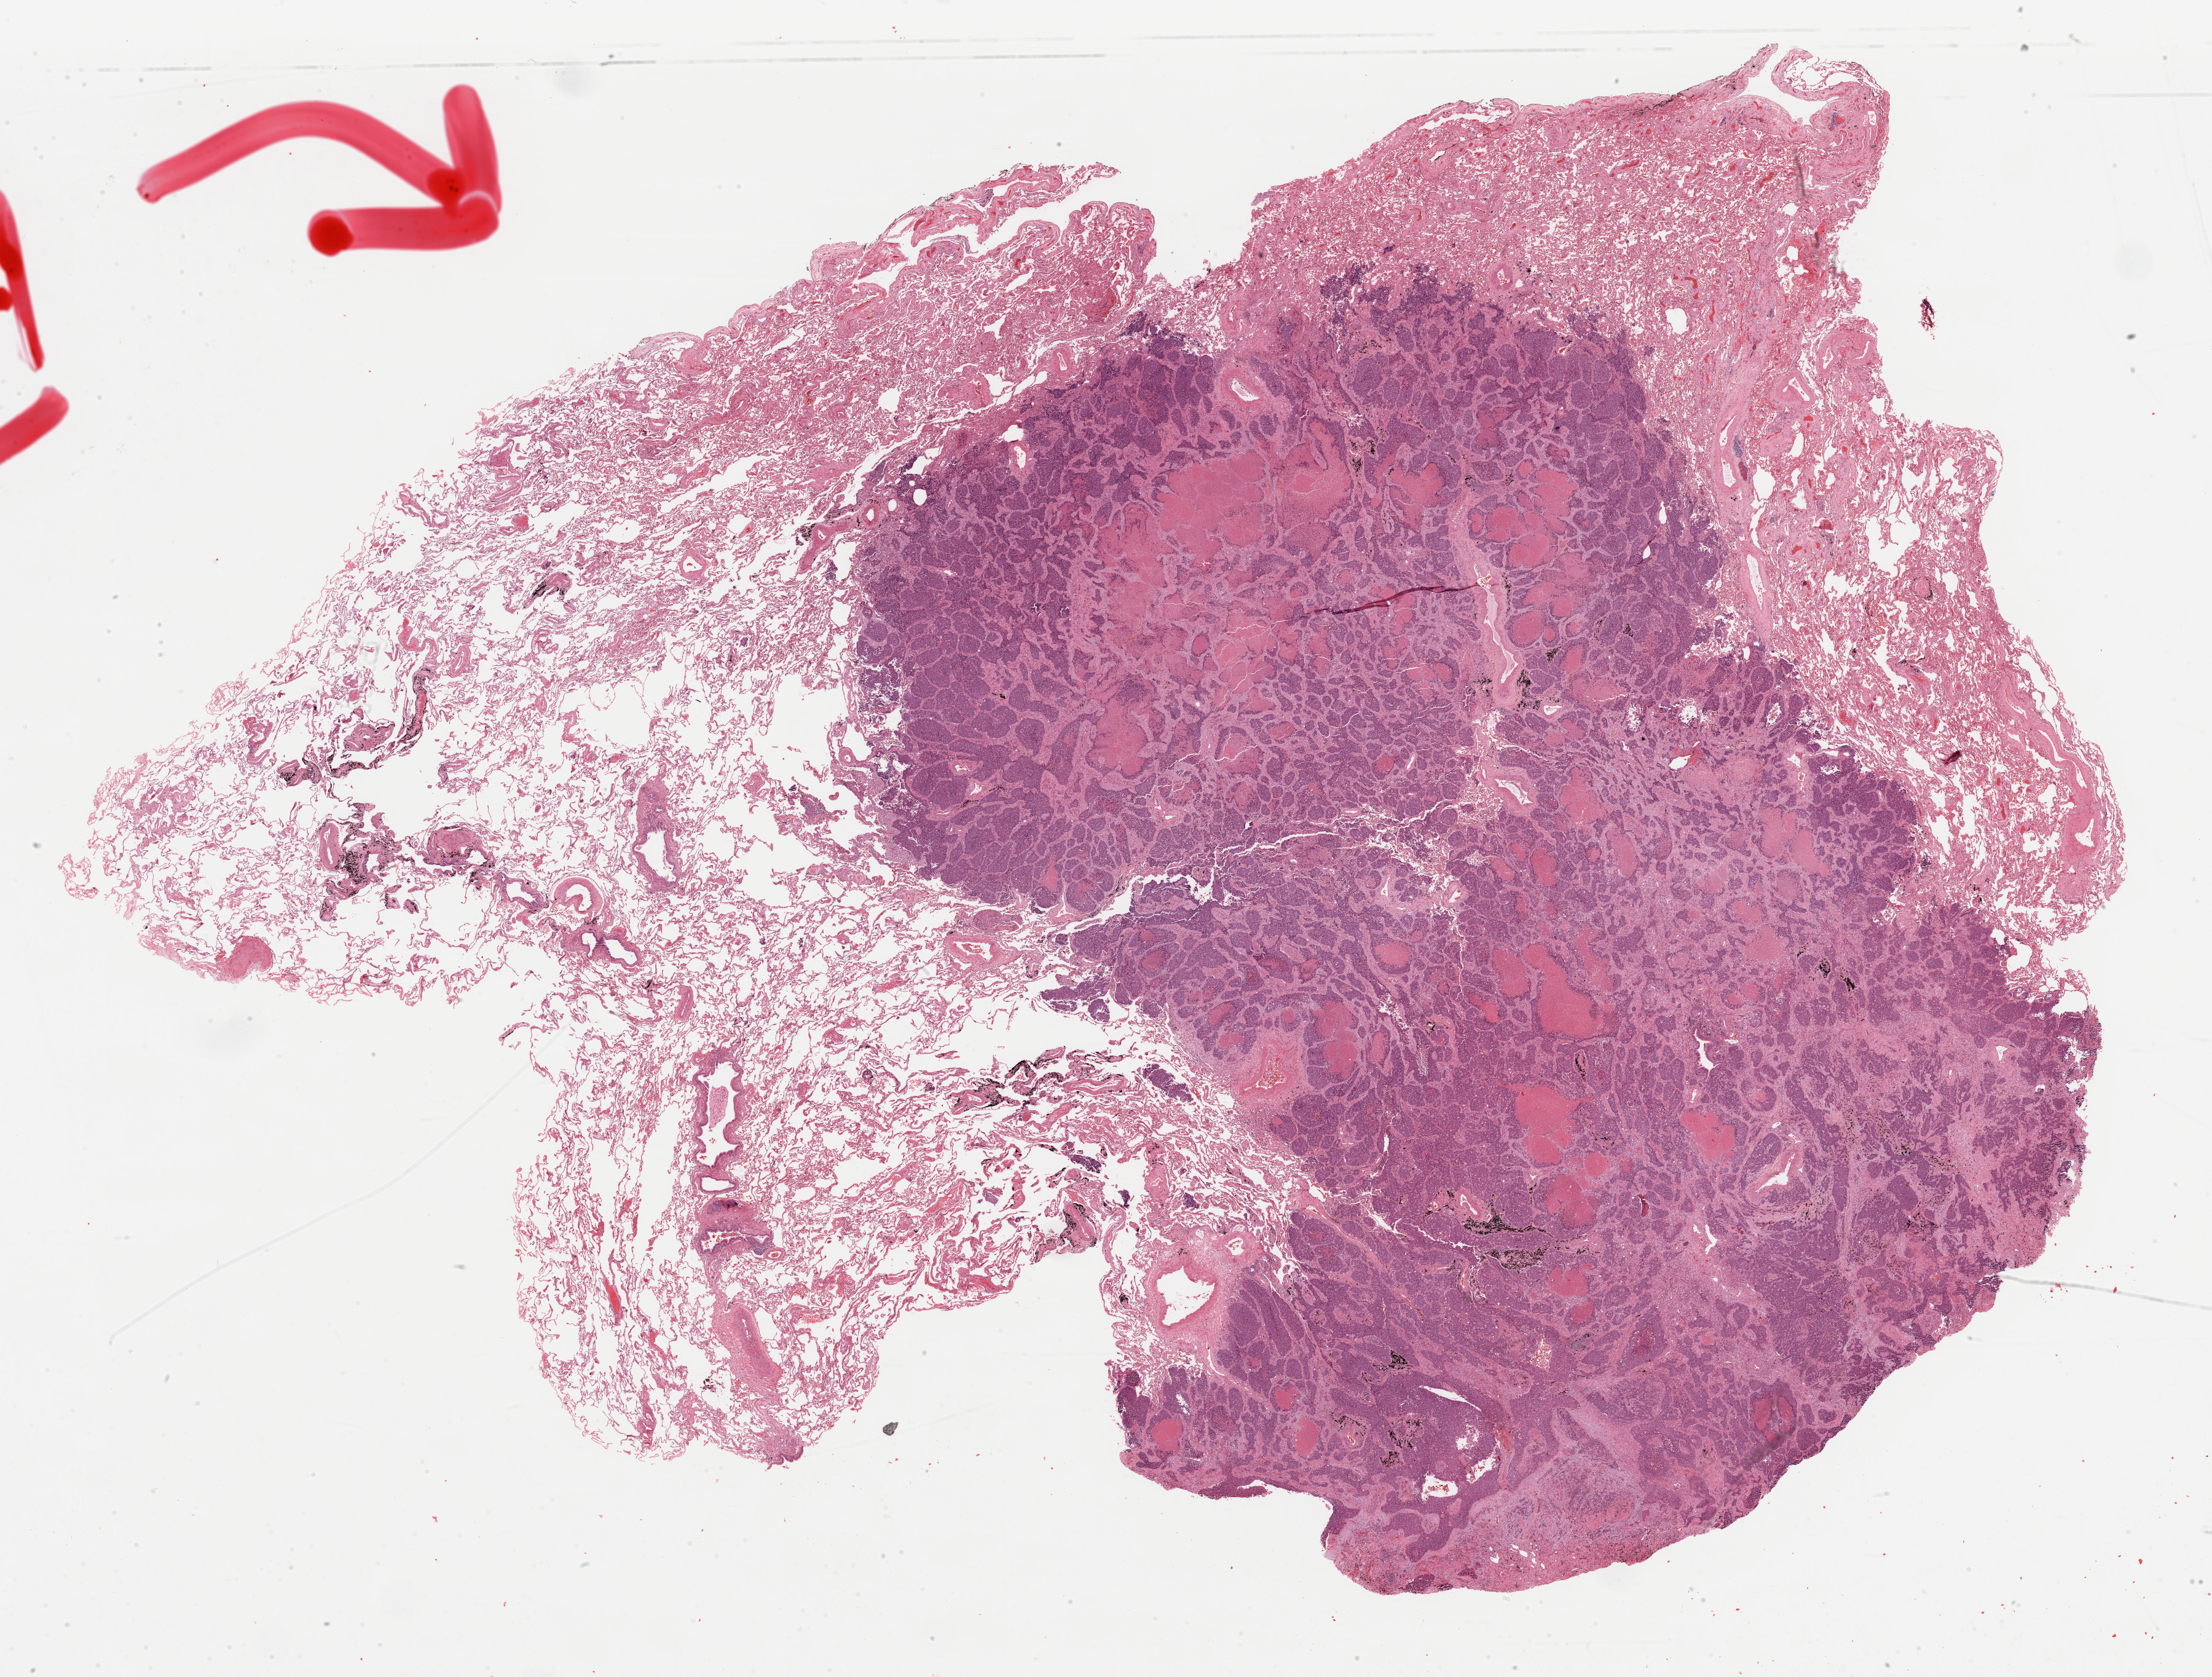
Hematoxylin and eosin (H&E) stained whole-slide image, a low-resolution overview of the entire scanned area, about 28.4 x 21.5 mm; formalin-fixed paraffin-embedded (FFPE) diagnostic section; sample: primary tumour, lung. Female patient; age at initial diagnosis 75 years.
TNM: T2 N0 M0. Pathologic diagnosis: Adenocarcinoma, NOS. Laterality: left. AJCC pathologic stage: IB (5th edition).